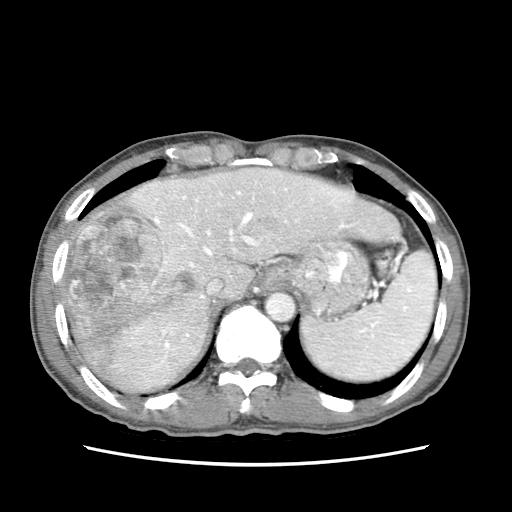
Contrast-enhanced abdominal CT (liver protocol), one axial slice. Position 57 of 79 along the scan axis. Reconstruction kernel STANDARD. Soft-tissue window (W 400 / L 40 HU). 2.5 mm slice thickness. 512 × 512 image matrix, field of view 320 × 320 mm. Case-level facts recorded for this patient, not image findings: diagnosis: hepatocellular carcinoma (patient treated with transarterial chemoembolisation; whether this scan precedes or follows treatment is not stated here); TNM stage (as recorded): Stage-IIIB.
Structures marked on this image (semi-automatic segmentation, software-assisted and operator-edited):
- abdominal aorta: bounding box (x1, y1, x2, y2) in pixels: (266, 293, 294, 322)
- liver parenchyma outside the tumour (the mass and vessels are separate outlines, so this box may not span the whole liver): (60, 168, 399, 392)
- mass: (62, 181, 196, 371)
- liver vessels: (138, 179, 337, 367)